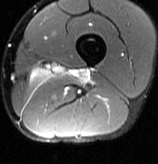
MRI of an extremity soft-tissue mass, one axial slice; slice 17 of 70 in the series (ordered by position); T2-weighted fat-saturated; MR volume resampled by the dataset authors to the PET/CT grid (not the native acquisition matrix); 3.27 mm slice thickness; 158 × 164 image matrix, field of view 154 × 160 mm. Male patient. From the clinical record (not read from this slice): histological type: extraskeletal osteosarcoma; grade: high; site of the primary tumour: left adductur.
Structures marked on this image (expert contour drawn on MRI and transferred to this co-registered scan by the dataset authors):
- gross tumour volume (mass): bounding box <70,69,89,81> (left, top, right, bottom; pixels)